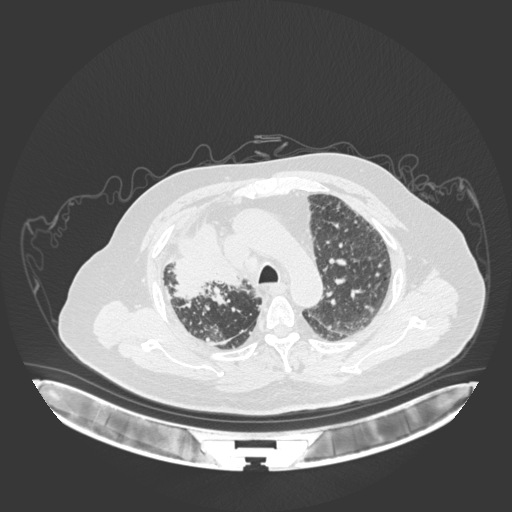
Chest CT, one axial slice; position 133 of 201 along the scan axis; 120 kVp; lung window (W 1500 / L -600 HU); 1 mm slice thickness; 512 × 512 image matrix, field of view 500 × 500 mm. Male patient, age 69 years. Case-level facts recorded for this patient, not image findings: clinical TNM (as recorded): T4 N3 M1.
Outlined on this slice (rectangle marked by the reading radiologist):
- lung tumour (recorded histology: adenocarcinoma): bounding box <166,225,248,305> (left, top, right, bottom; pixels)